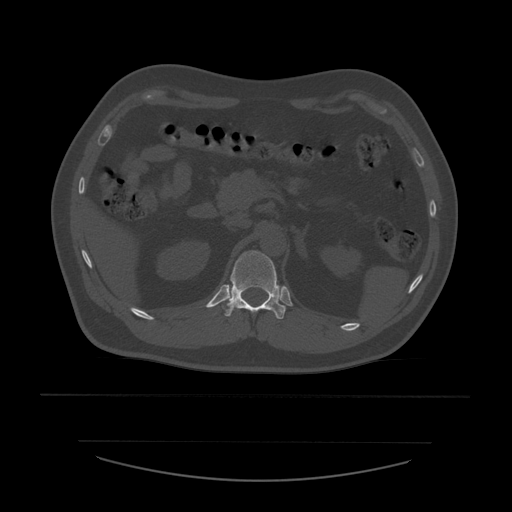
CT including the spine, one axial slice. Slice 251 of 532 in the series (ordered by position). 120 kVp. Bone window (W 1800 / L 400 HU). 512 × 512 image matrix, field of view 441 × 441 mm. Patient age 44 years. From the clinical record (not read from this slice): primary cancer: soft tissue sarcoma.
Outlined on this slice (semi-automatically segmented with operator editing):
- T12 vertebra: box from (x=223, y=251) to (x=286, y=319) px